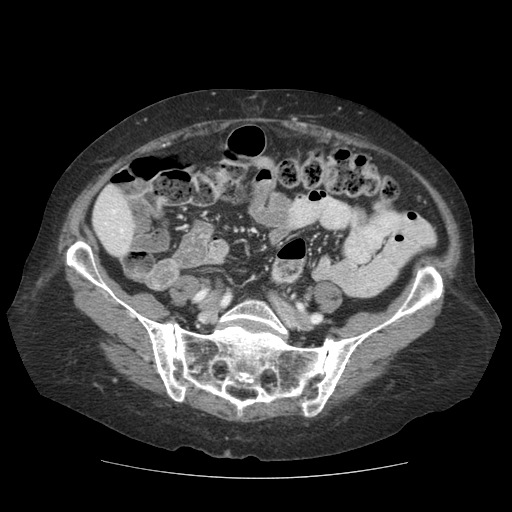
Contrast-enhanced abdominal CT (liver protocol), one axial slice; slice 16 of 111 in the series (ordered by position); soft-tissue window (W 400 / L 40 HU); 512 × 512 image matrix, field of view 360 × 360 mm. Case-level facts recorded for this patient, not image findings: diagnosis: hepatocellular carcinoma (patient treated with transarterial chemoembolisation; whether this scan precedes or follows treatment is not stated here); TNM stage (as recorded): Stage-I; Child-Pugh class: A; tumour size: 7.3 cm.
Outlined on this slice (semi-automatically segmented with operator editing):
- liver parenchyma outside the tumour (the mass and vessels are separate outlines, so this box may not span the whole liver): box from (x=92, y=184) to (x=134, y=256) px
- liver vessels: (x=105, y=210)–(x=123, y=233)